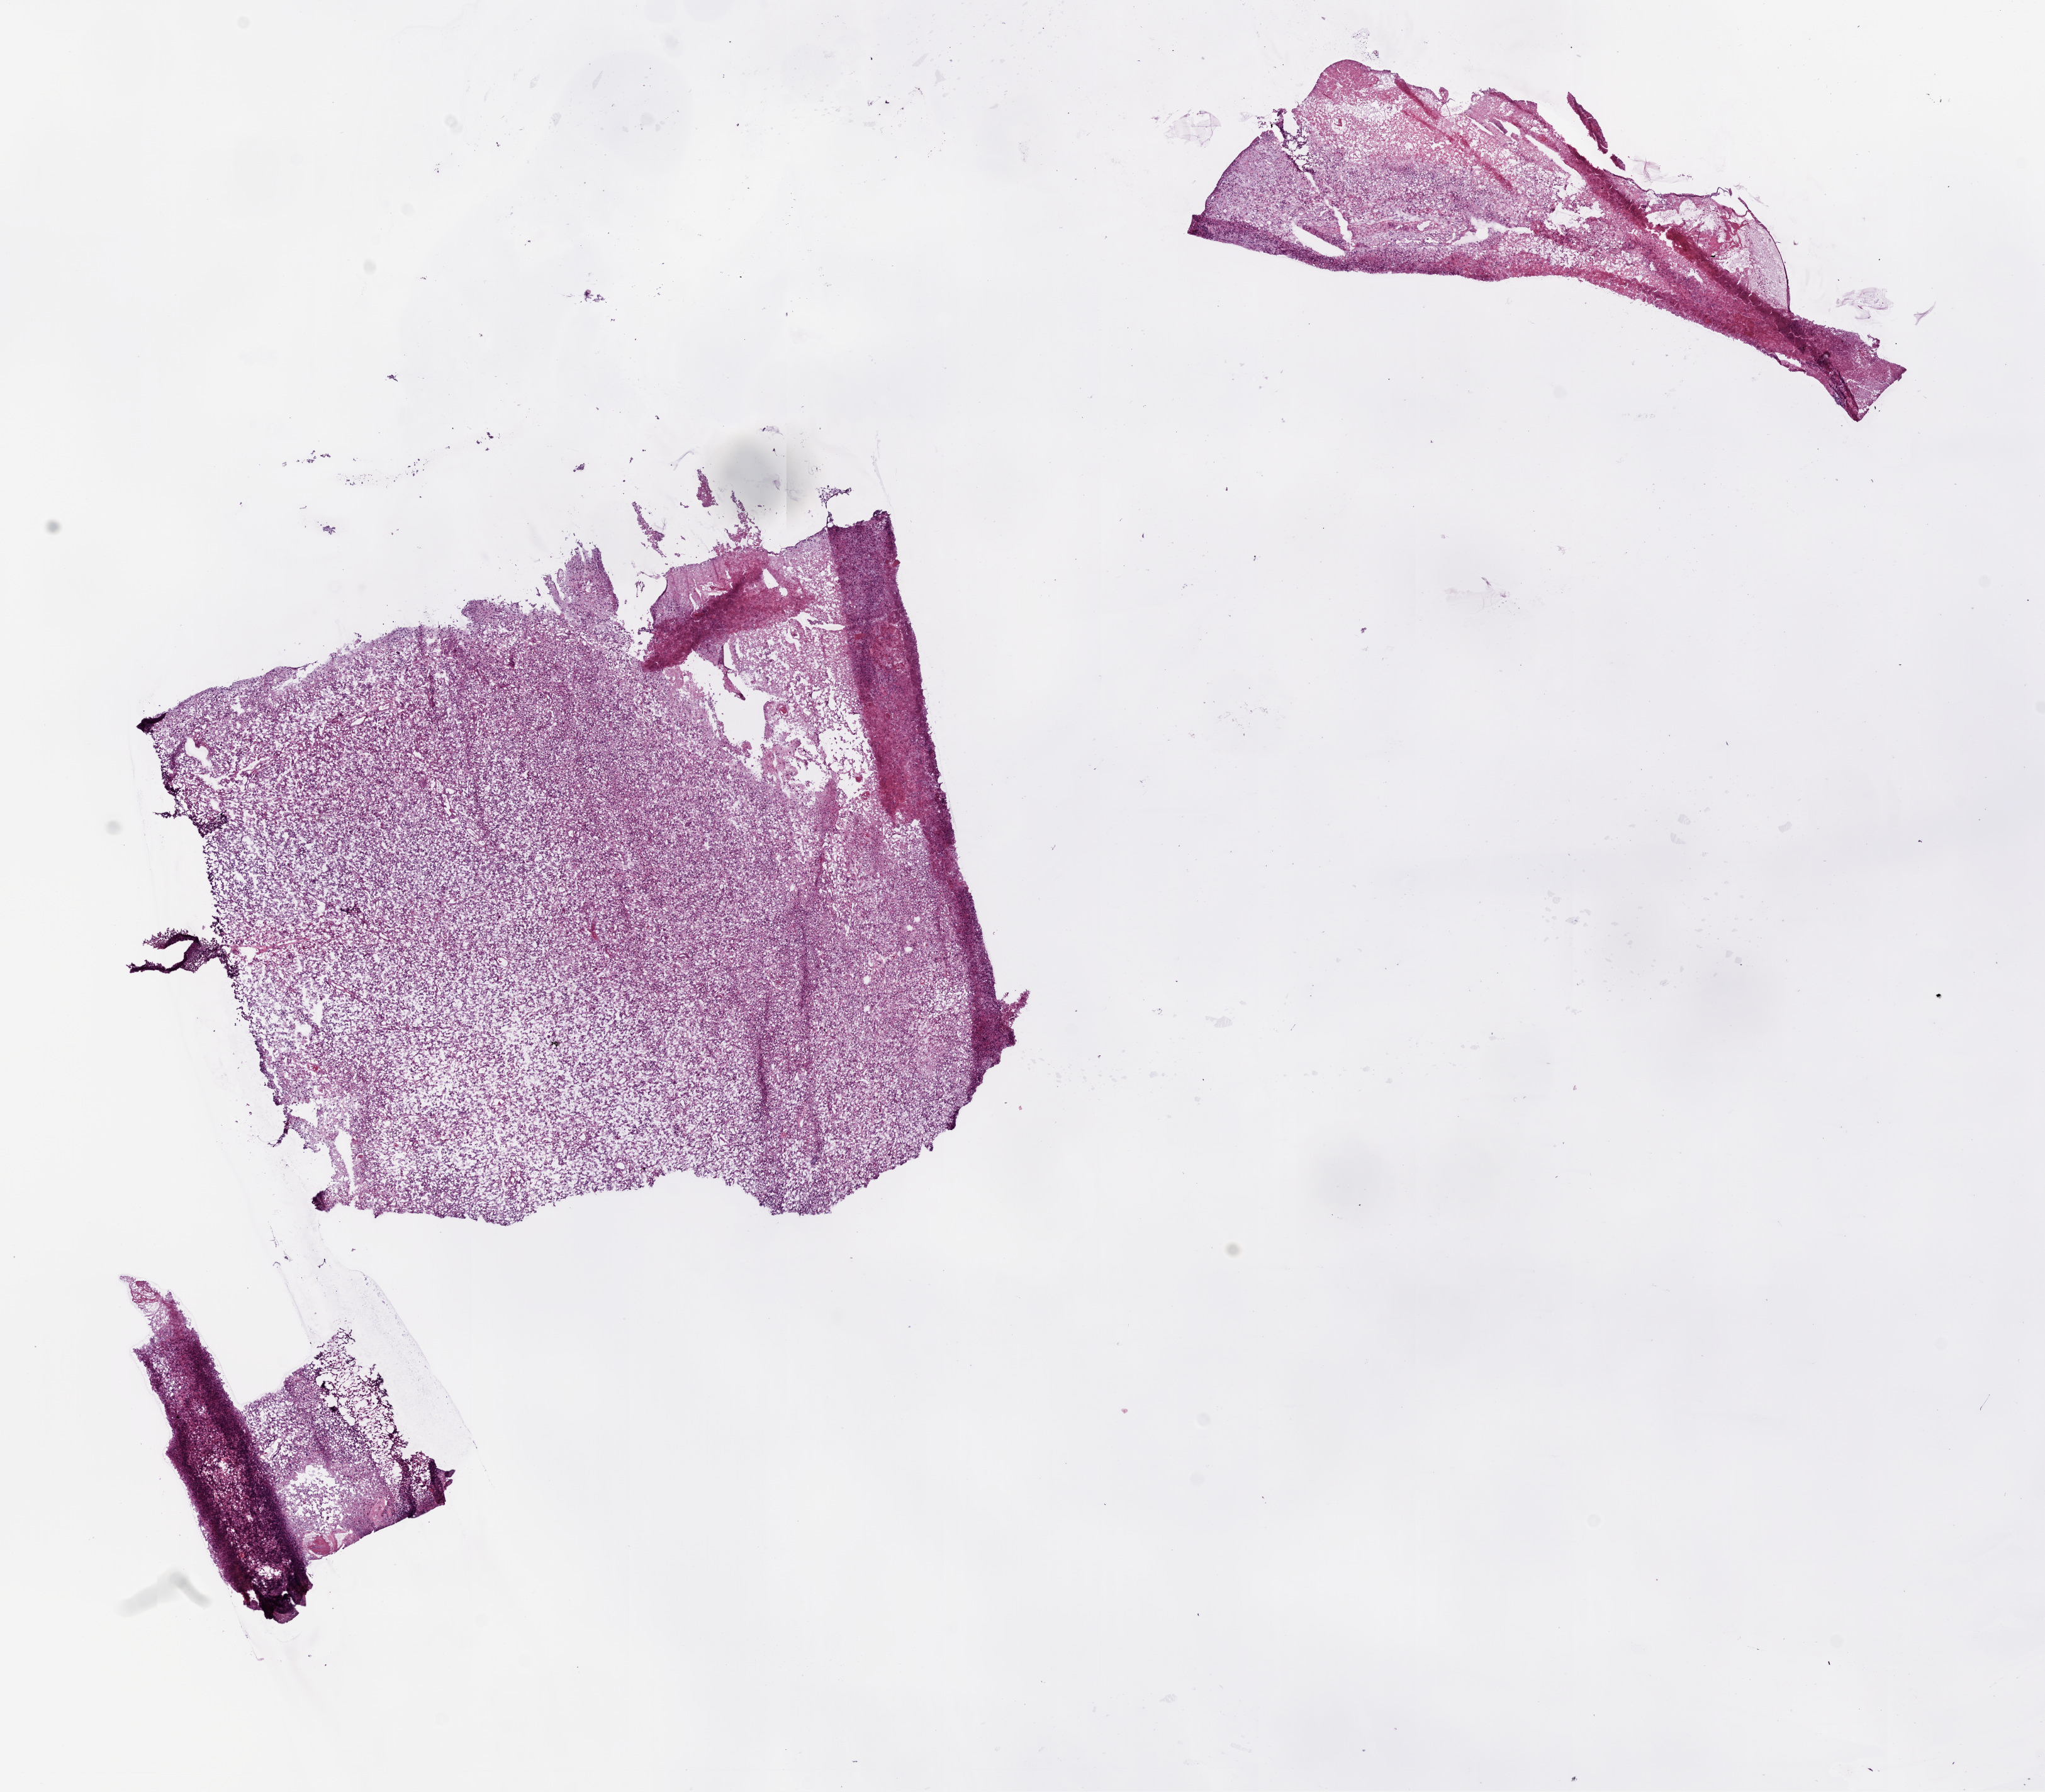
Whole-slide histology image, H&E-stained, shown as a low-resolution overview of the whole scanned area (about 13.0 x 11.4 mm). Frozen section from the bottom of the tissue portion. Primary tumour sample from the brain. Patient: female, age at initial diagnosis 56 years. Pathologist review of this section (percent, as recorded): tumour cells 85%, tumour nuclei 80%, normal cells 0%, stromal cells 0%, necrosis 15%.
Pathologic diagnosis: Glioblastoma.